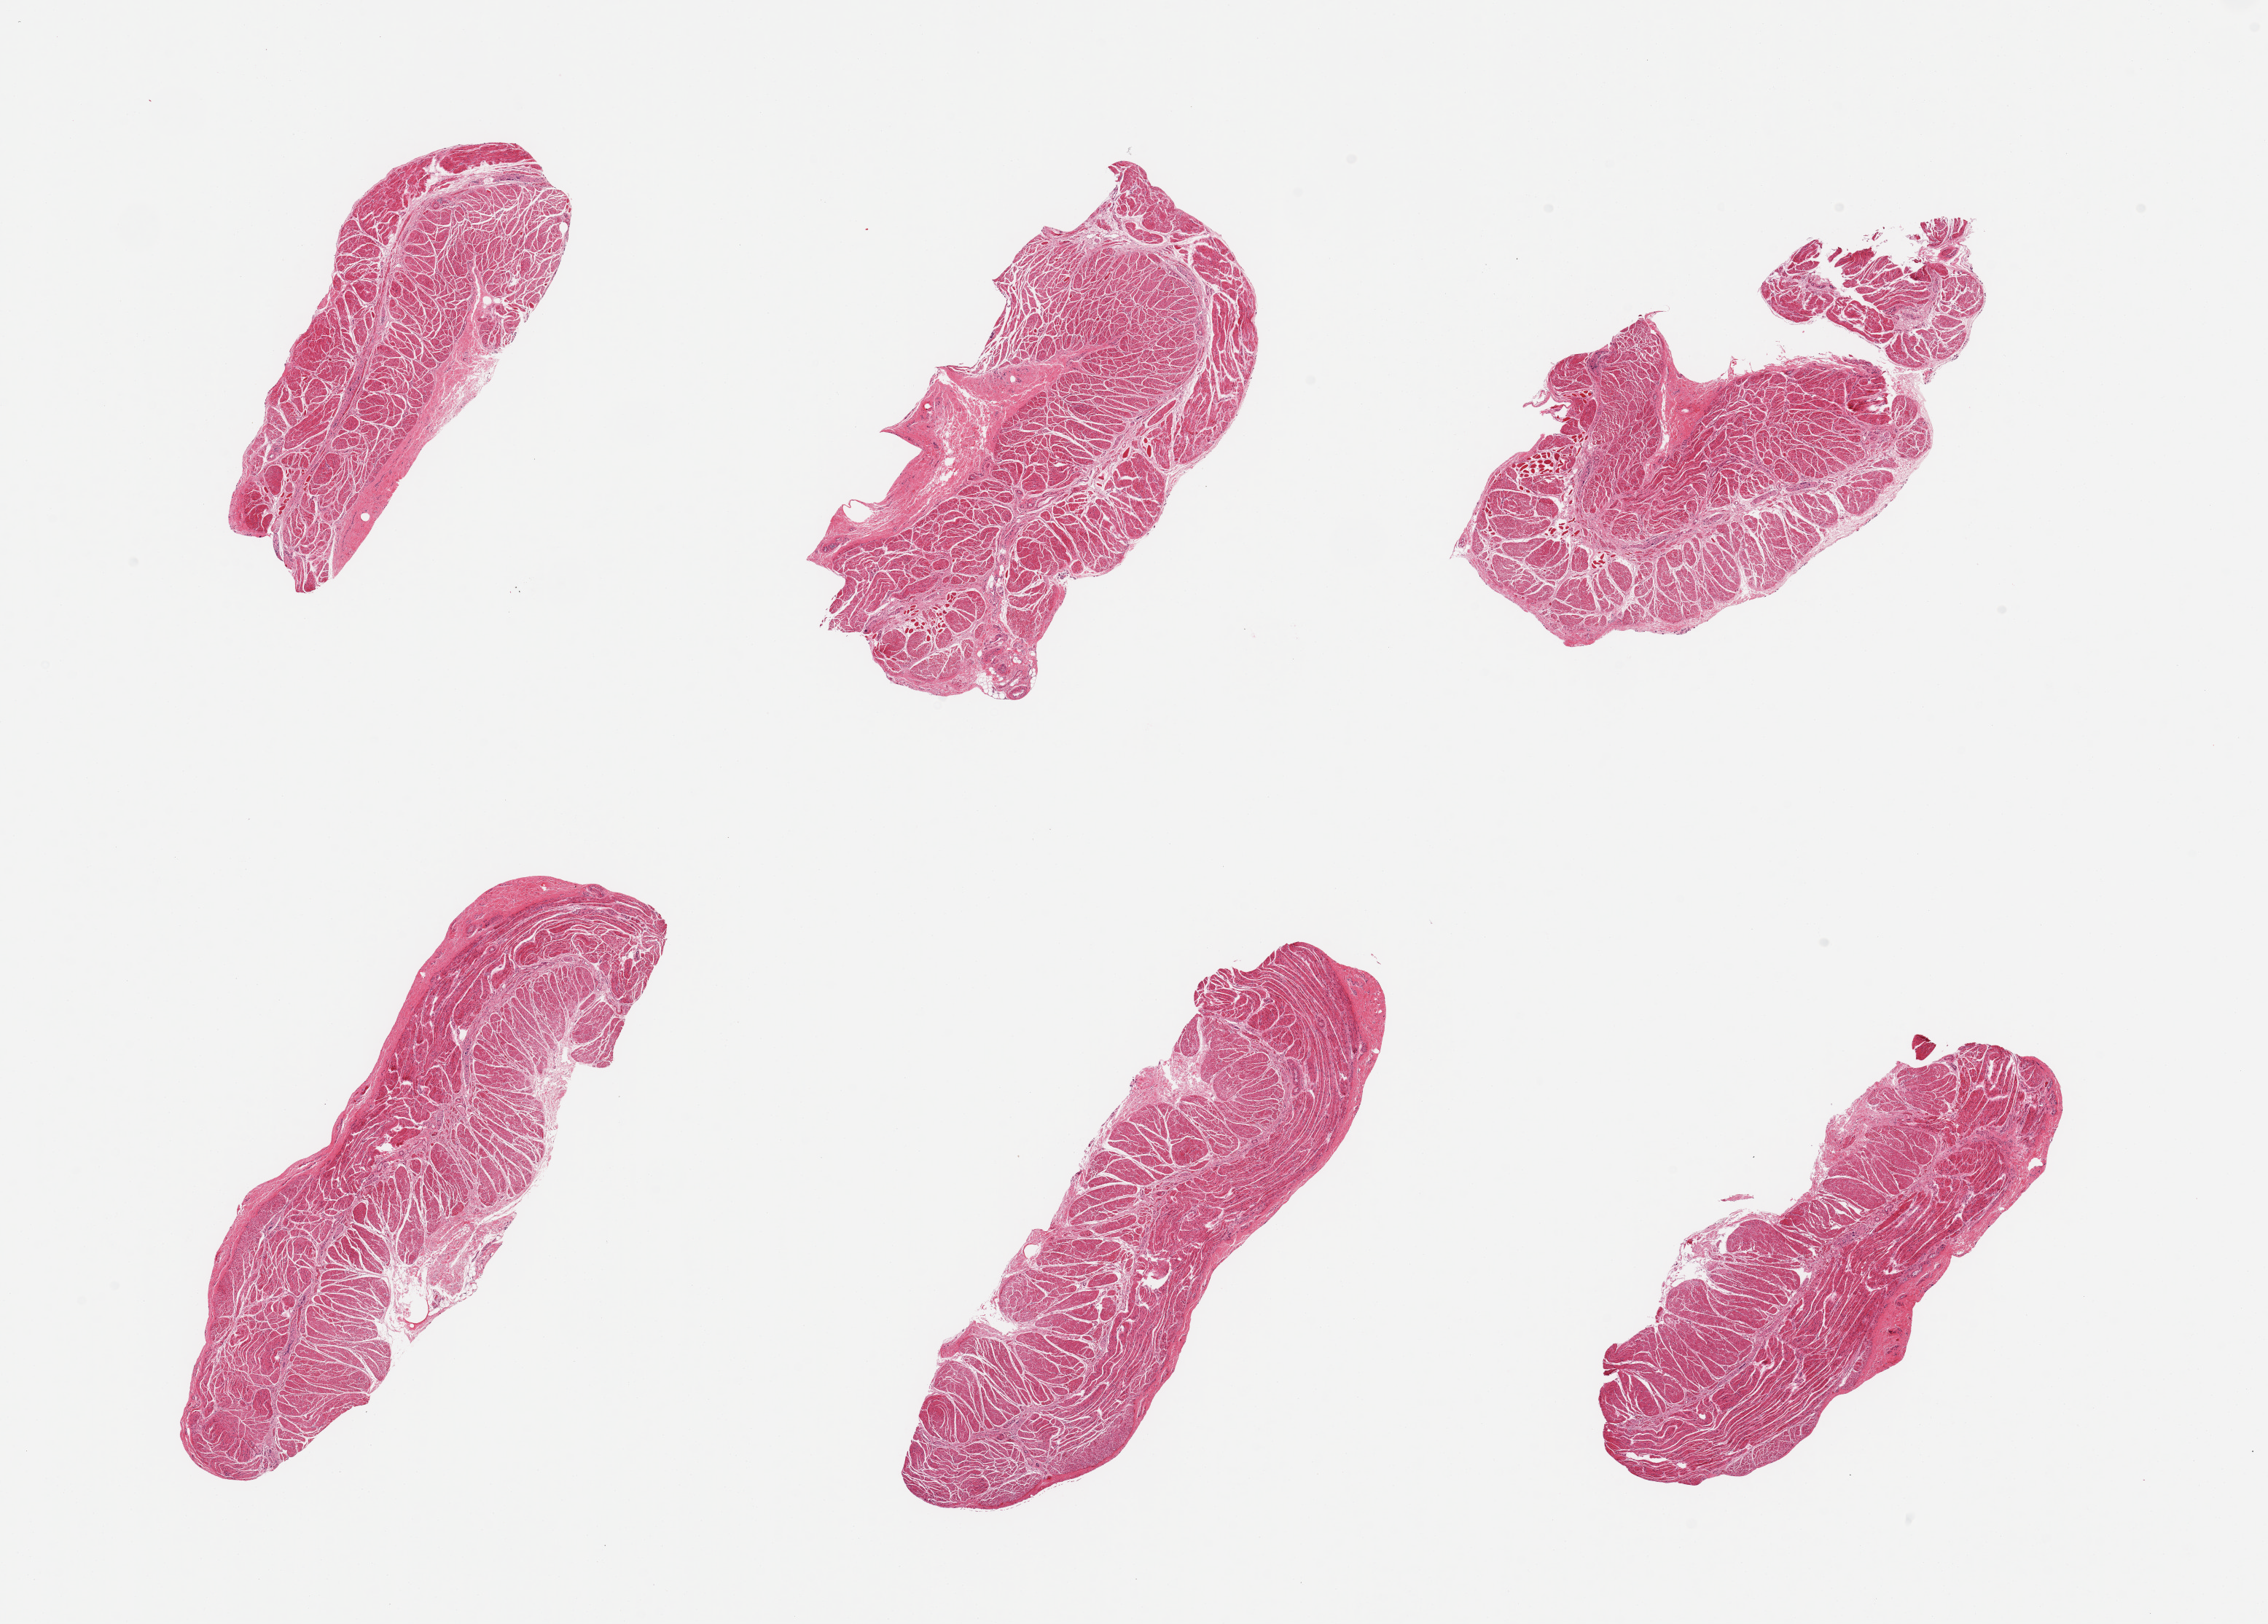
Whole-slide image, hematoxylin and eosin (H&E) stain — low-resolution overview of the scanned area, about 24.6 x 17.6 mm (slide scanned at 20x). PAXgene-fixed, paraffin-embedded tissue. Sampled site (target tissue): esophageal muscle. Donor tissue sample. Donor: female.
Reviewer comment on this tissue sample: 6 pieces, confirmed target muscularis.